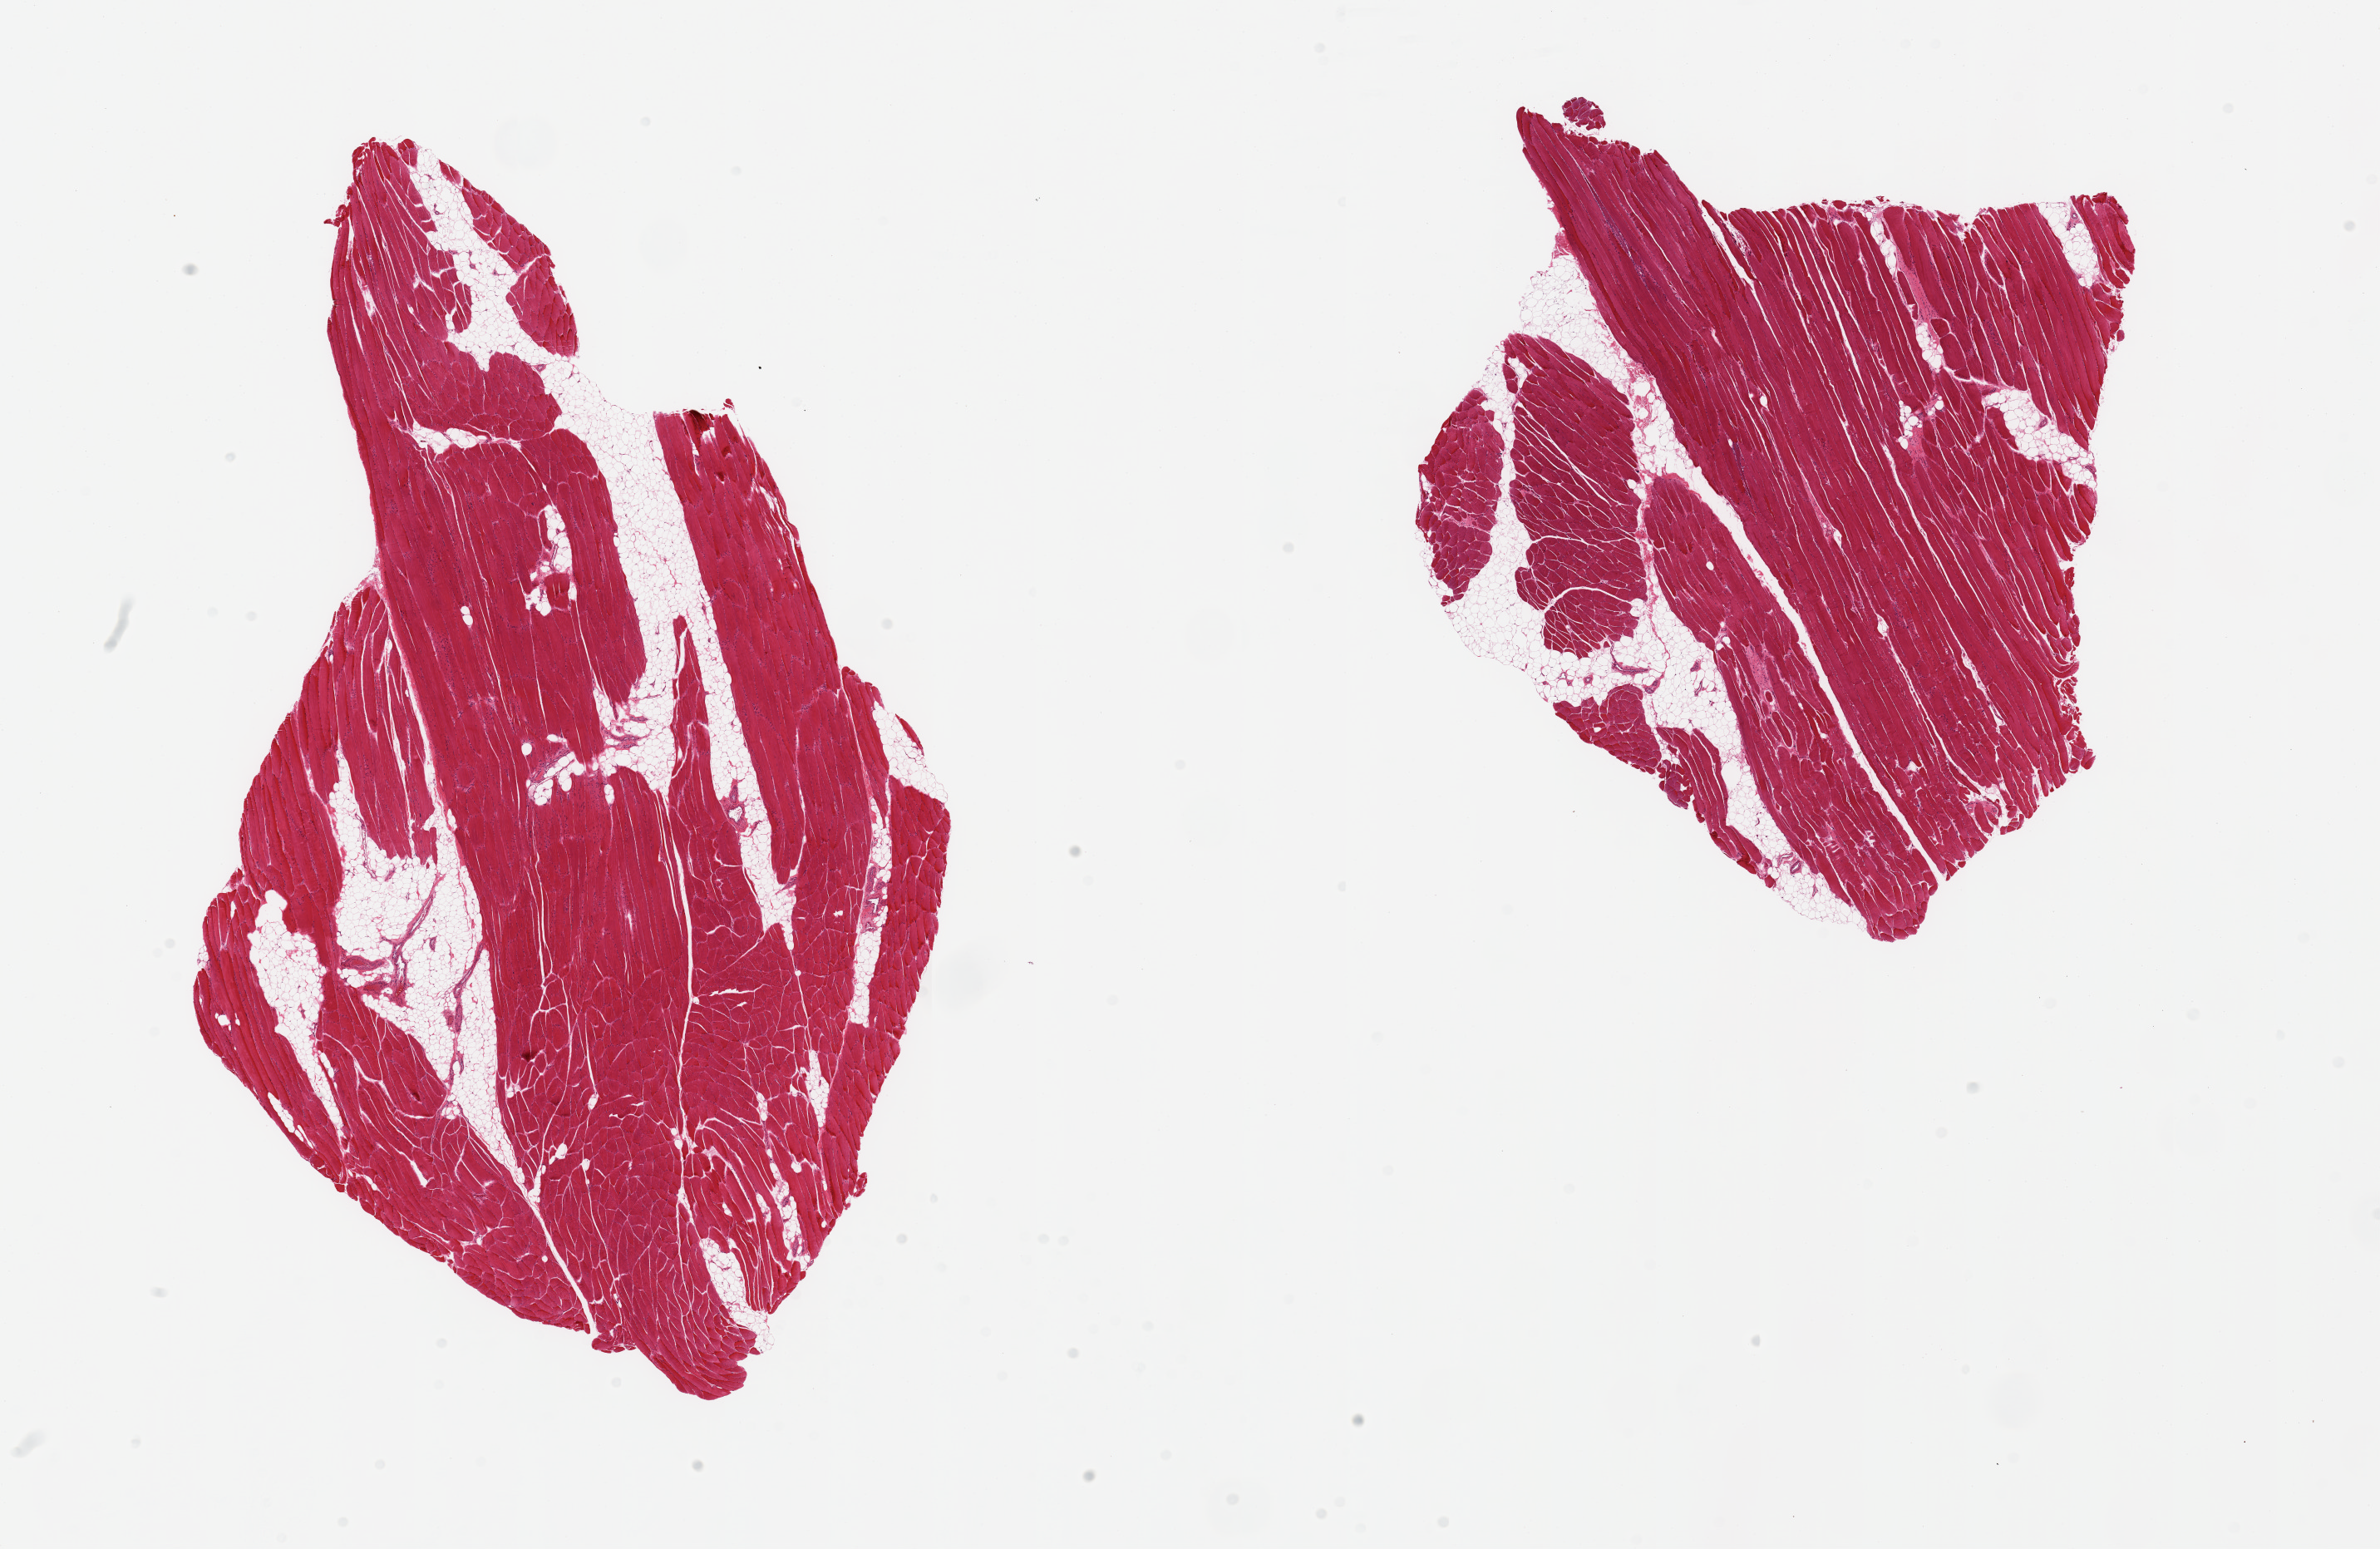
Digitized H&E-stained section — a low-resolution overview of the entire scanned area, about 22.6 x 14.7 mm (slide scanned at 20x). PAXgene-fixed, paraffin-embedded tissue. Section of skeletal muscle (target tissue). Donor tissue sample.
• reviewer comment on this tissue sample: 2 pieces; 10 & 20% internal fat